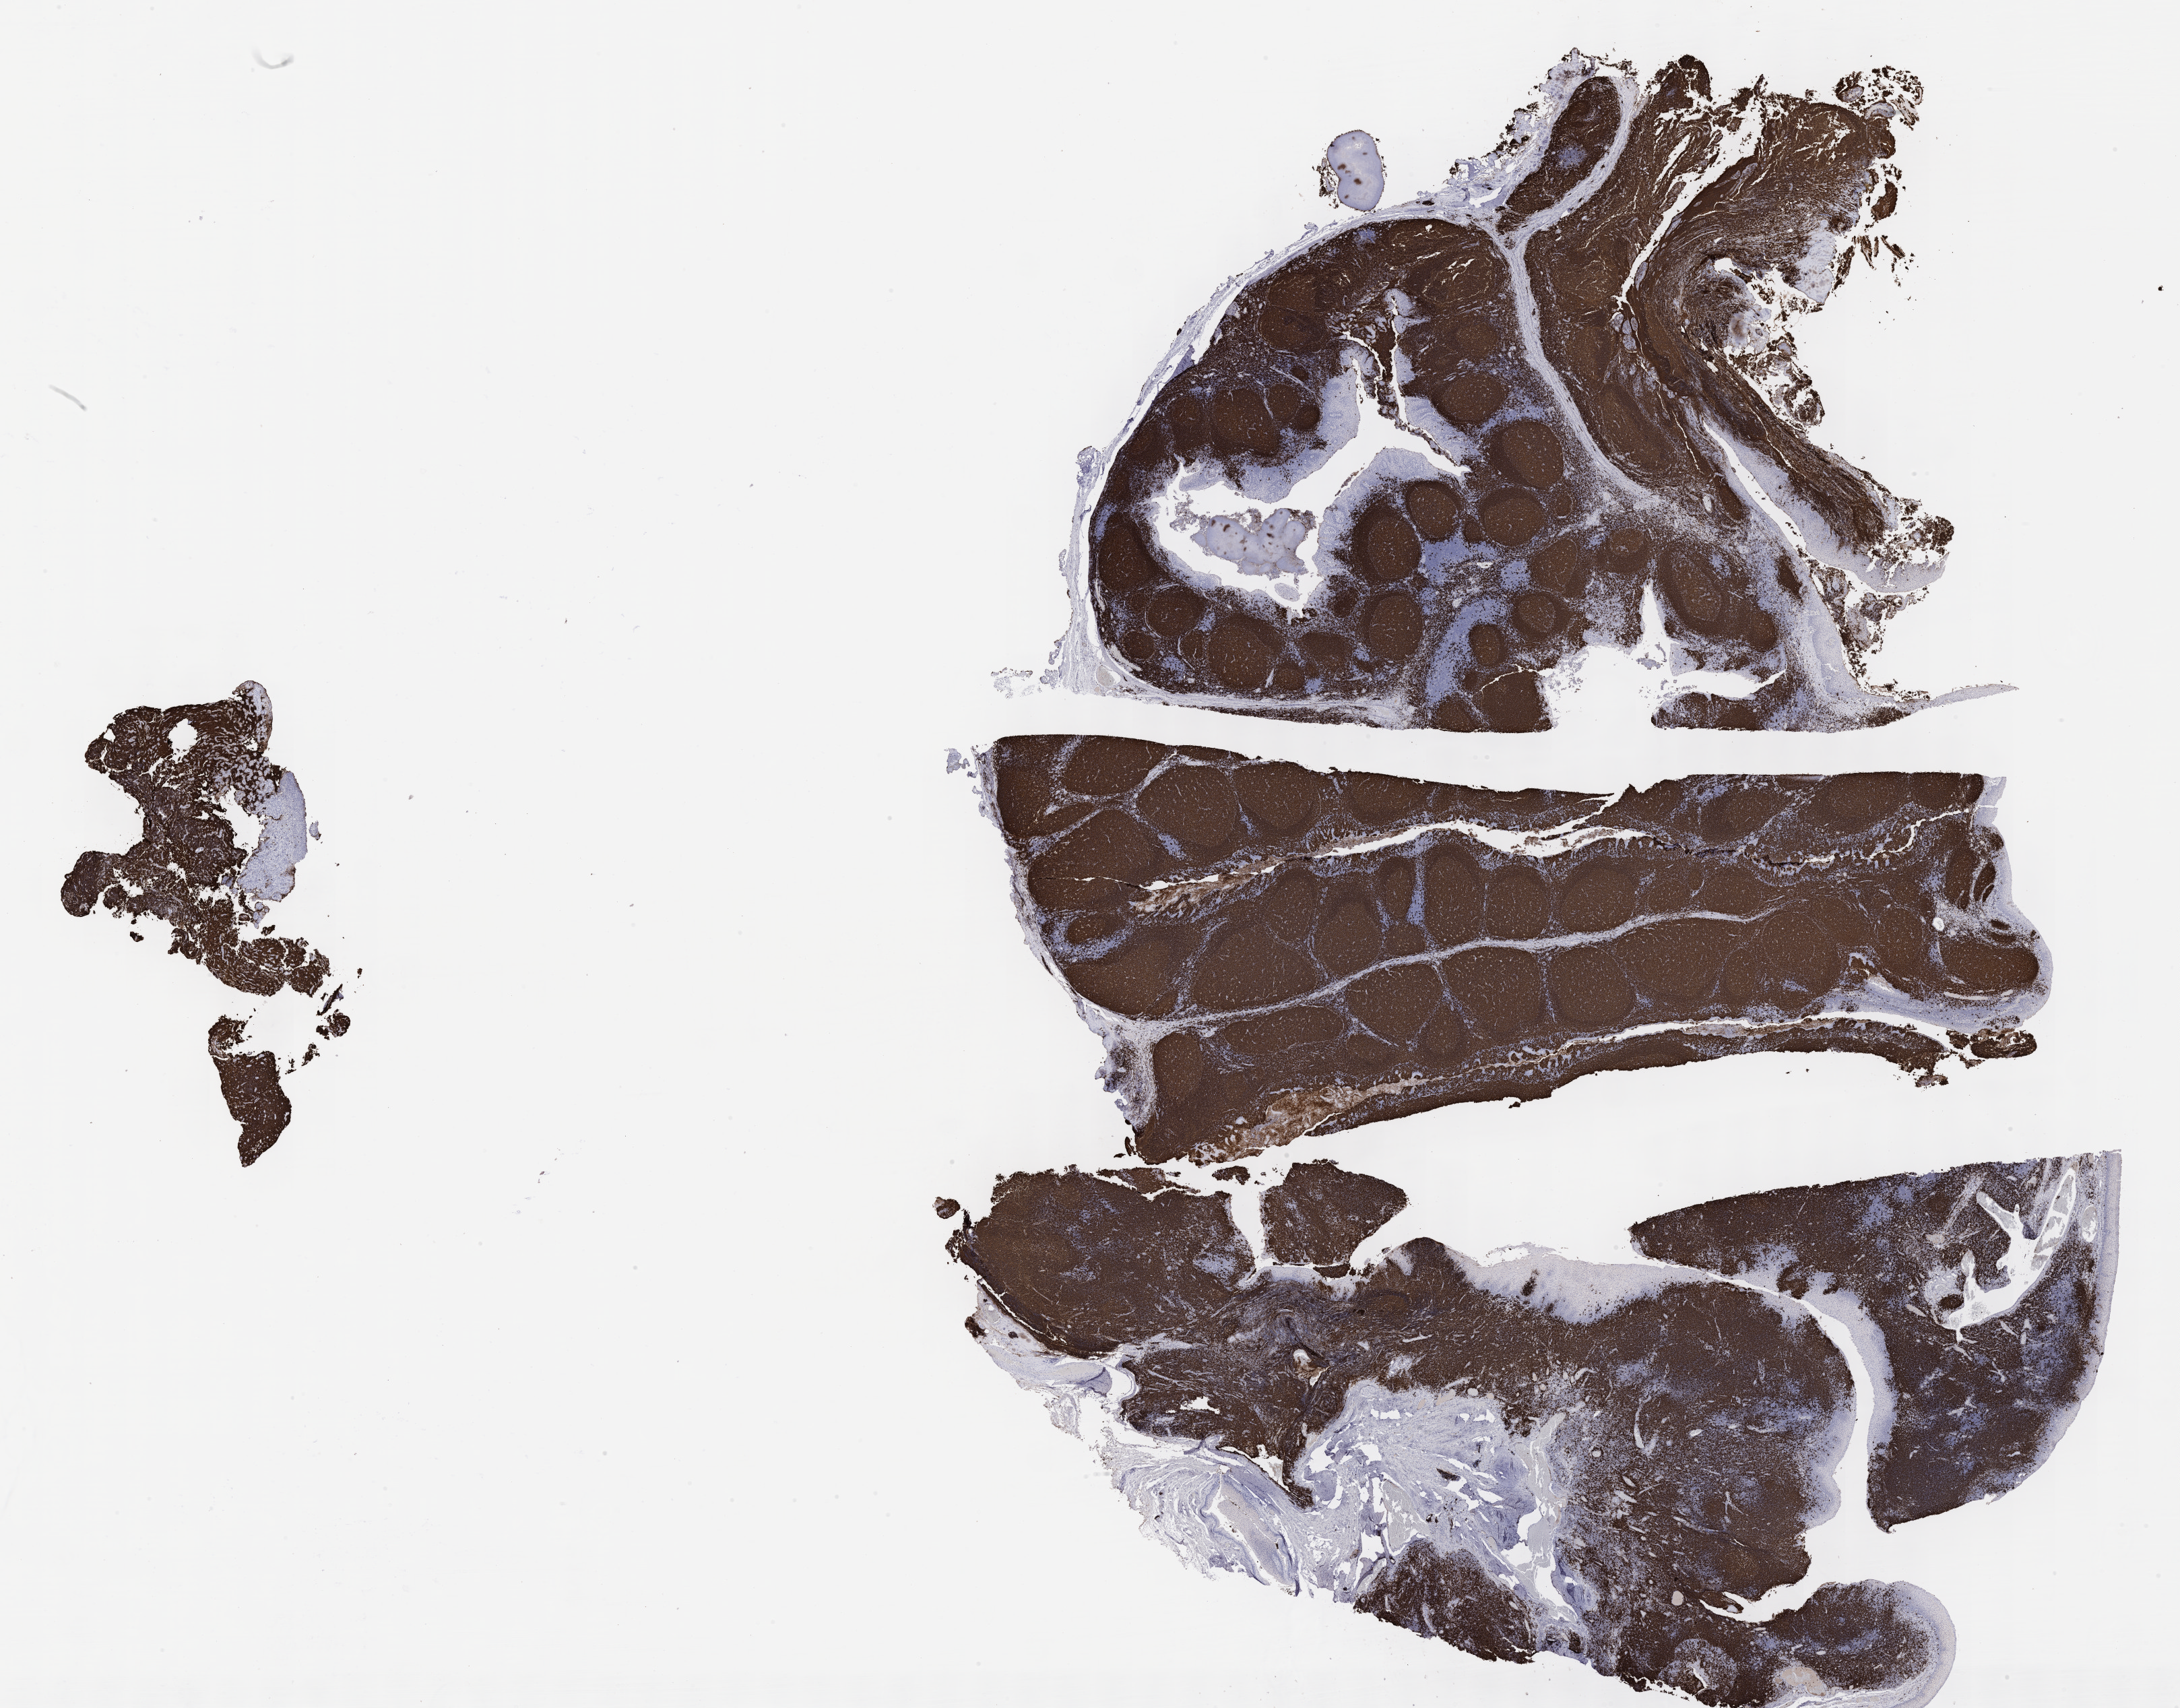
IHC for CD20, whole-slide image, shown as a low-resolution overview of the whole scanned area (about 26.2 x 20.5 mm). Specimen: tumor tissue. Anatomic site: gum of mandible. Patient male; aged 10.
Histologic diagnosis: Burkitt lymphoma, NOS.